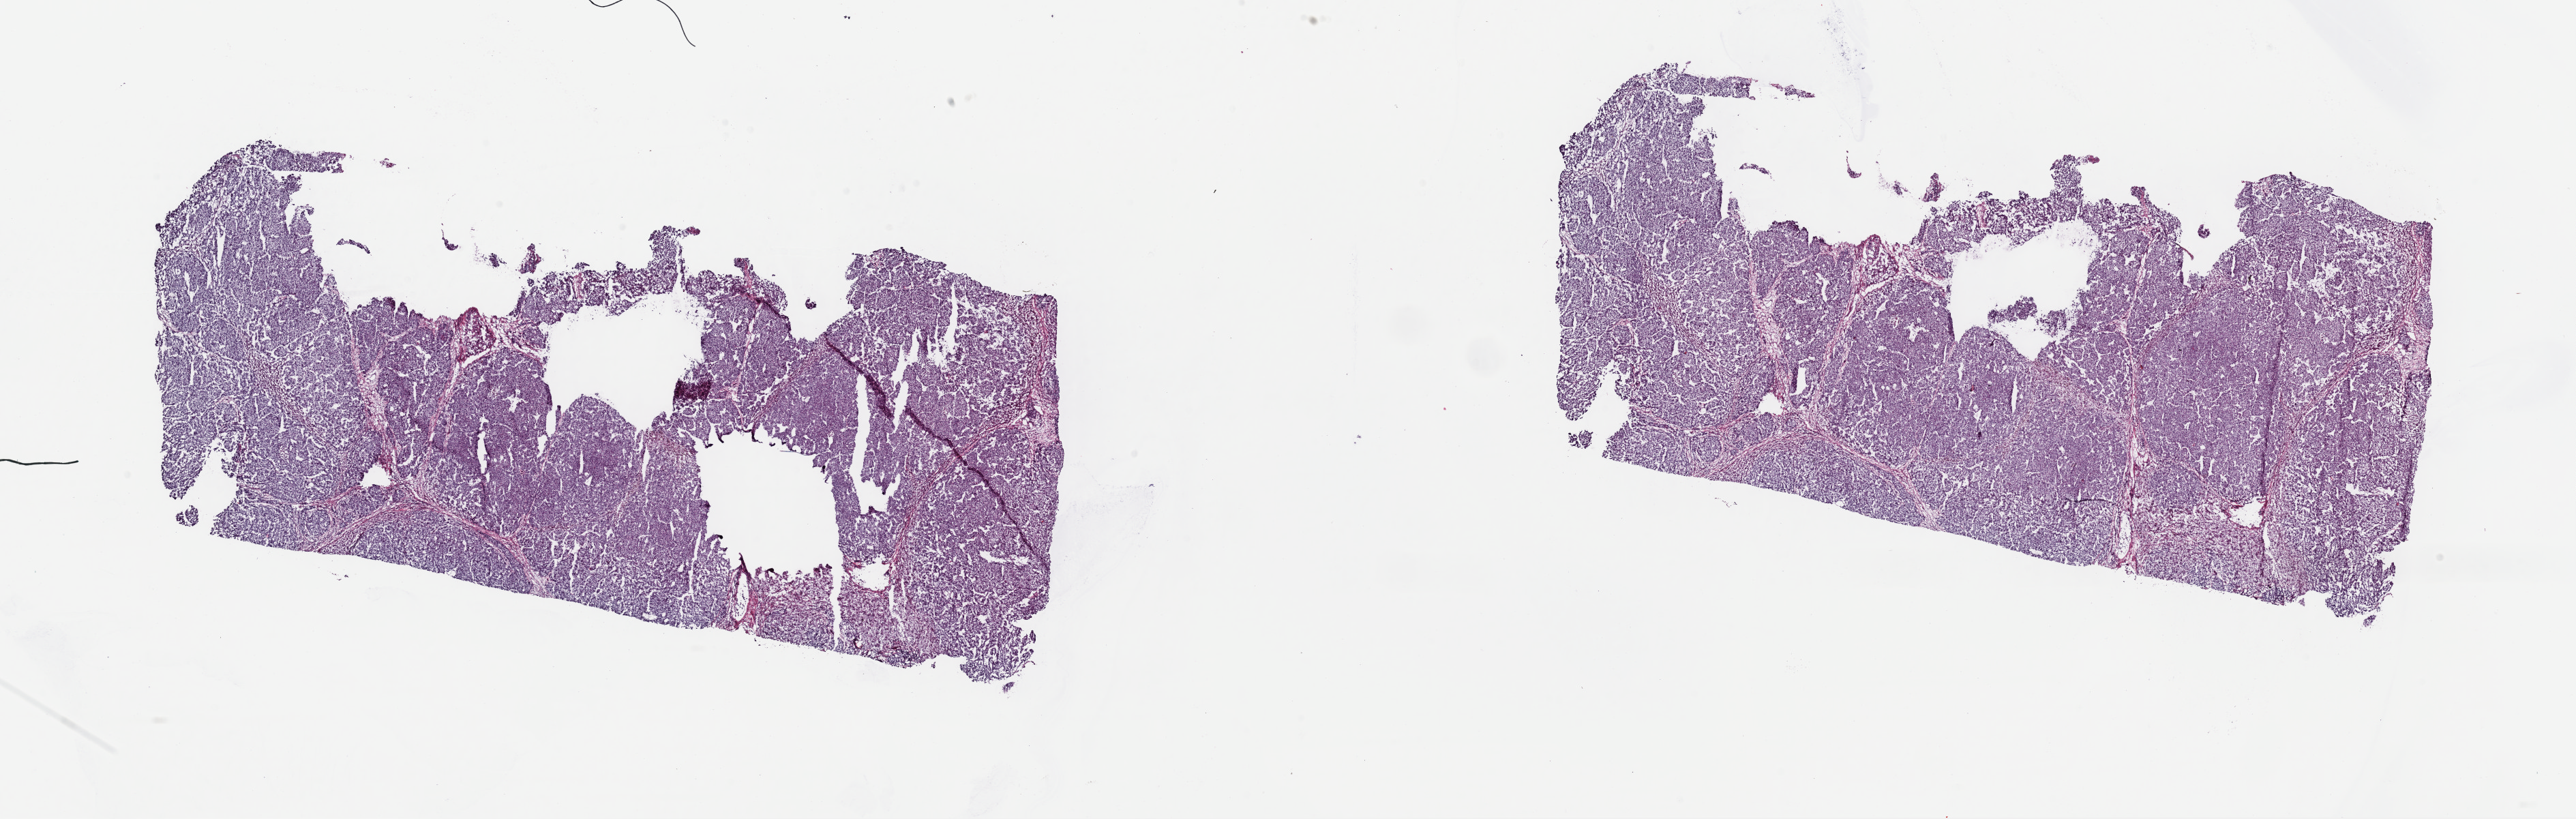
Whole-slide histology image, H&E, whole scanned area (about 29.8 x 9.5 mm) shown as a low-resolution overview. Frozen section from the top of the tissue portion. Primary tumour sample from the liver. Patient: male, age at initial diagnosis 36 years. Composition of this section per pathologist review: tumour cells 85%, tumour nuclei 85%.
Pathologic diagnosis: Hepatocellular carcinoma, NOS.